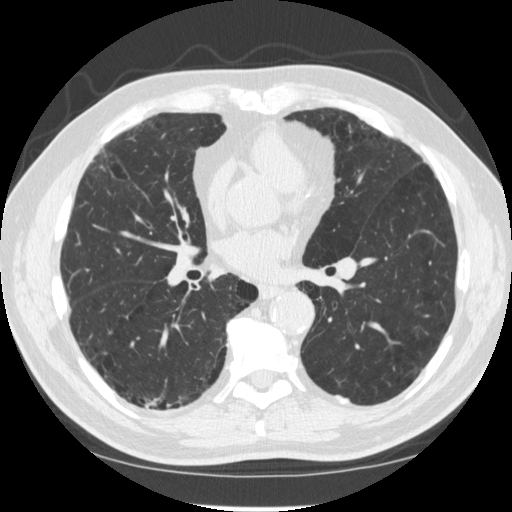
Chest CT (low-dose screening protocol), one axial image. Second screening round (one year after baseline). Lung window (W 1500 / L -600 HU). 1.25 mm slice thickness. Standard (soft-tissue) reconstruction kernel (STANDARD). Male, age 70 years at enrolment.
Lesion marked by an expert reader, bounding box (x1, y1, x2, y2) in pixels: (133, 379, 186, 429). The screening reader recorded 2 non-calcified nodules or masses ≥4 mm on this exam; which of them this box marks is not recorded.